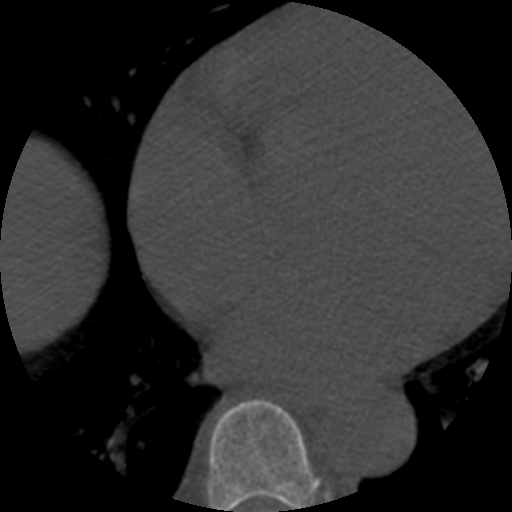
CT including the spine, one axial slice. Slice 329 of 508 in the series (ordered by position). Bone window (W 1800 / L 400 HU). 1.25 mm slice thickness. 512 × 512 image matrix. Patient age 57 years. From the clinical record (not read from this slice): primary cancer: prostate.
Outlined on this slice (semi-automatic segmentation, software-assisted and operator-edited):
- T7 vertebra: bounding box (x1, y1, x2, y2) in pixels: (207, 399, 319, 512)